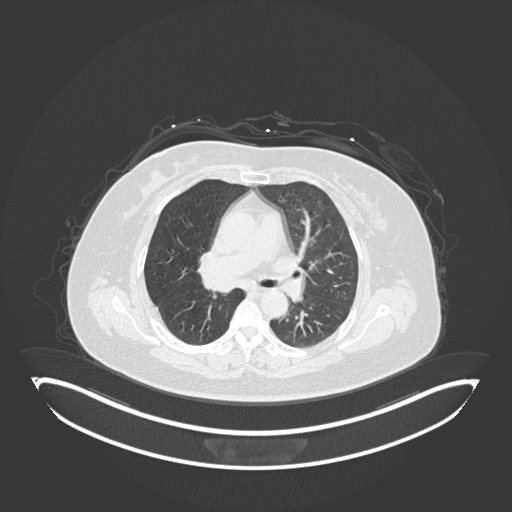
Chest CT, one axial slice; slice 97 of 245 in the series (ordered by position); lung window (W 1500 / L -600 HU); 1 mm slice thickness; 512 × 512 image matrix, field of view 500 × 500 mm. Female patient, age 60 years. Case-level facts recorded for this patient, not image findings: clinical TNM (as recorded): T1c N0 M0; histopathological grade: G1-G2.
Structures marked on this image (bounding box drawn by a radiologist):
- lung tumour (recorded histology: squamous cell carcinoma): bounding box (x1, y1, x2, y2) in pixels: (205, 274, 242, 297)